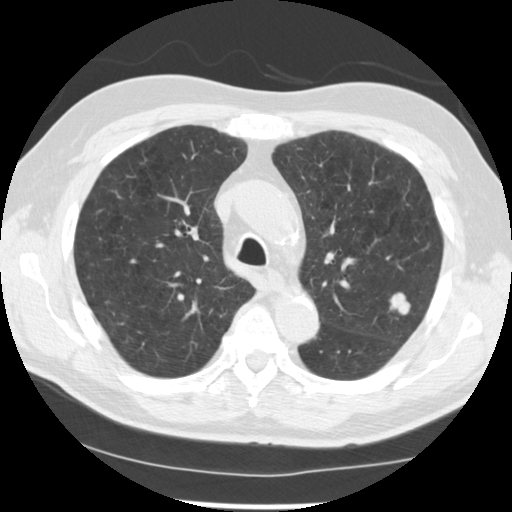
Low-dose screening chest CT, one axial slice. Position 173 of 249 along the scan axis. Reconstruction kernel STANDARD. 120 kVp. Lung window (W 1500 / L -600 HU). 512 × 512 image matrix, field of view 341 × 341 mm.
Annotated regions visible in this slice (expert manual segmentation):
- lesion 1 (tumor, upper lobe of left lung): bounding box [x1, y1, x2, y2] px = [390, 293, 410, 315]